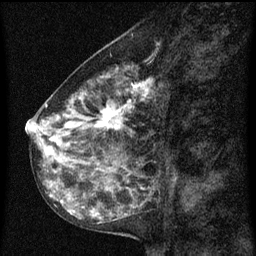
Breast MRI (dynamic contrast-enhanced), one sagittal slice; slice 33 of 60 in the series (ordered by position); dynamic contrast-enhanced series, image 2 of 3 at this slice position (ordered by acquisition); 1.5 T; TE 4.2 ms, TR 8 ms; 2 mm slice thickness; 256 × 256 image matrix, field of view 180 × 180 mm. Female patient, age 55 years.
Annotated regions visible in this slice (semi-automatic segmentation, software-assisted and operator-edited):
- analysis volume of interest (the breast-tissue region the enhancement analysis was run in; not a lesion): box from (x=34, y=68) to (x=157, y=151) px
- tumour enhancement mask (voxels above the 70 % enhancement threshold inside the analysis volume of interest): (x=40, y=72)–(x=151, y=149)